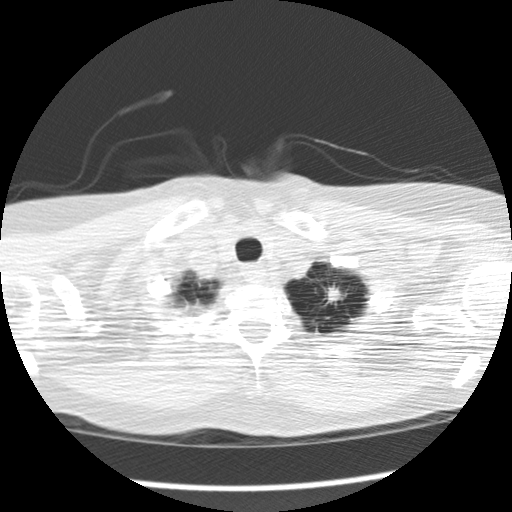
Low-dose screening chest CT, one axial slice; position 150 of 159 along the scan axis; 120 kVp; lung window (W 1500 / L -600 HU); 2.5 mm slice thickness; 512 × 512 image matrix, field of view 308 × 308 mm.
Structures marked on this image (manually delineated by an expert):
- lesion 1 (tumor, upper lobe of left lung): bounding box (x1, y1, x2, y2) in pixels: (327, 286, 343, 303)